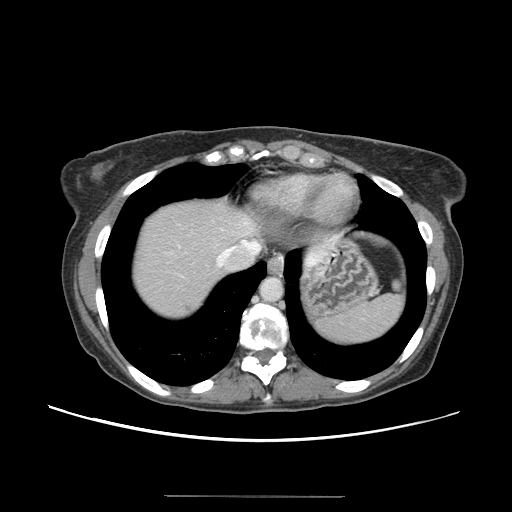
Contrast-enhanced abdominal CT, one axial slice; position 128 of 144 along the scan axis; 120 kVp; intravenous contrast given; soft-tissue window (W 400 / L 40 HU); 512 × 512 image matrix. Female patient, age 53 years. Case-level facts recorded for this patient, not image findings: diagnosis: colorectal cancer liver metastases, imaged before liver resection; multiple liver metastases: yes; largest metastasis: 1.1 cm; disease in both lobes: no.
Outlined on this slice (expert manual segmentation):
- hepatic veins: bounding box (x1, y1, x2, y2) in pixels: (217, 240, 261, 266)
- liver: (131, 201, 257, 318)
- planned liver remnant (the part of the liver to remain after resection): (131, 198, 256, 292)
- liver metastasis: (185, 306, 191, 311)